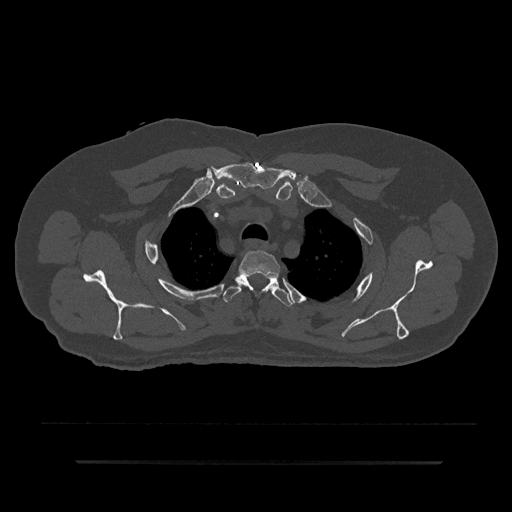
CT including the spine, one axial slice; 120 kVp; bone window (W 1800 / L 400 HU); 0.5 mm slice thickness; 512 × 512 image matrix, field of view 464 × 464 mm. Patient: male, 59 years. Case-level facts recorded for this patient, not image findings: primary cancer: bile ducts.
Structures marked on this image (semi-automatically segmented with operator editing):
- T2 vertebra: bounding box <239,251,280,293> (left, top, right, bottom; pixels)
- T3 vertebra: <222,274,294,307>